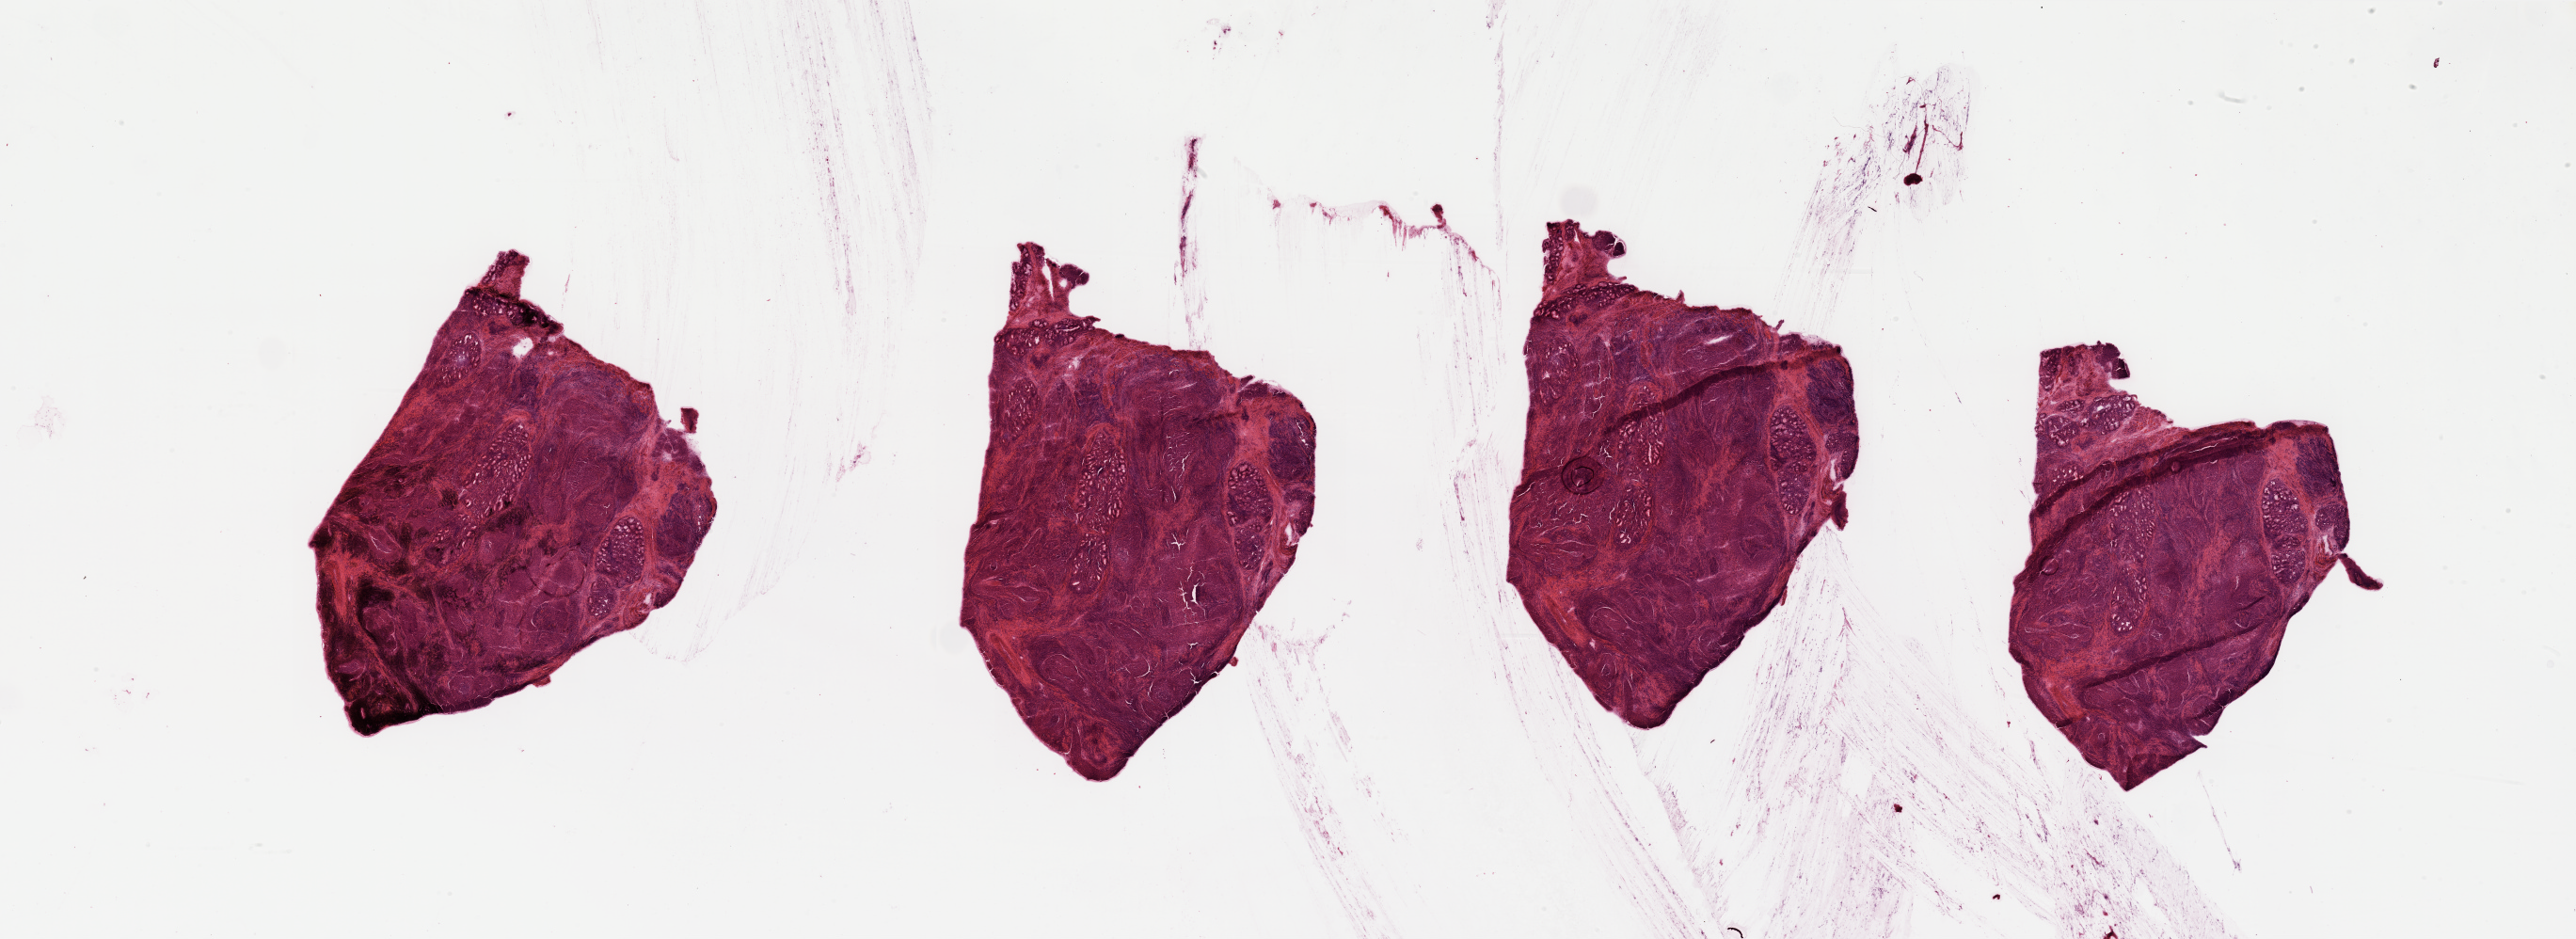
Whole-slide histology image, H&E-stained — shown as a low-resolution overview of the whole scanned area (about 43.3 x 15.8 mm), tumour tissue sample, sampled site: larynx. 67-year-old male patient. Histologic grade: G2 (moderately differentiated). Composition of this section per pathologist review: tumour nuclei 80%, necrosis 10%.
Diagnosis: Squamous cell carcinoma, NOS (larynx, NOS). Primary tumour site (as recorded): larynx. AJCC pathologic stage: II.